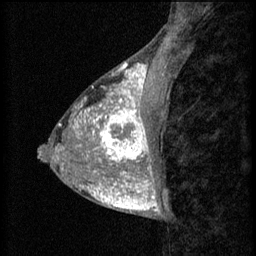
Breast MRI (dynamic contrast-enhanced), one sagittal slice. Slice 22 of 60 in the series (ordered by position). 3 images stored at this slice position (order not interpretable as contrast timing). 1.5 T. TE 4.2 ms, TR 8.2 ms. 2 mm slice thickness. 256 × 256 image matrix, field of view 180 × 180 mm. Patient: female, 38 years.
Structures marked on this image (semi-automatic segmentation, software-assisted and operator-edited):
- analysis volume of interest (the breast-tissue region the enhancement analysis was run in; not a lesion): bounding box <95,106,157,171> (left, top, right, bottom; pixels)
- tumour enhancement mask (voxels above the 70 % enhancement threshold inside the analysis volume of interest): <95,106,152,171>